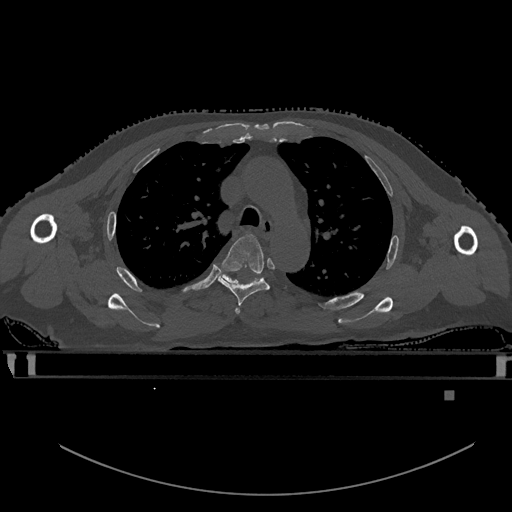
CT including the spine, one axial slice. Position 400 of 969 along the scan axis. Bone window (W 1800 / L 400 HU). 512 × 512 image matrix, field of view 456 × 456 mm. Patient: male, 82 years. From the clinical record (not read from this slice): primary cancer: prostate; vertebrae with lytic lesions (as recorded): T11, T9, T8, T2.
Structures marked on this image (semi-automatic segmentation, software-assisted and operator-edited):
- T3 vertebra: bounding box [x1, y1, x2, y2] px = [235, 308, 240, 314]
- T4 vertebra: [218, 234, 269, 308]
- T5 vertebra: [216, 271, 261, 284]